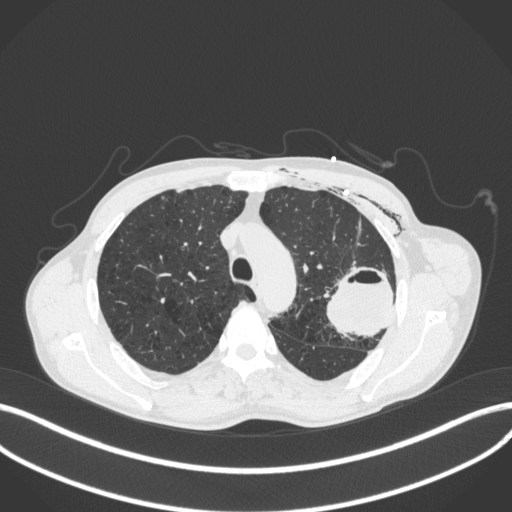
Chest CT, one axial slice. Position 300 of 416 along the scan axis. Lung window (W 1500 / L -600 HU). 1 mm slice thickness. 512 × 512 image matrix, field of view 400 × 400 mm. Male patient, age 58 years. From the clinical record (not read from this slice): clinical TNM (as recorded): T3 N0 M0.
Structures marked on this image (bounding box drawn by a radiologist):
- lung tumour (recorded histology: adenocarcinoma): box from (x=318, y=264) to (x=401, y=339) px